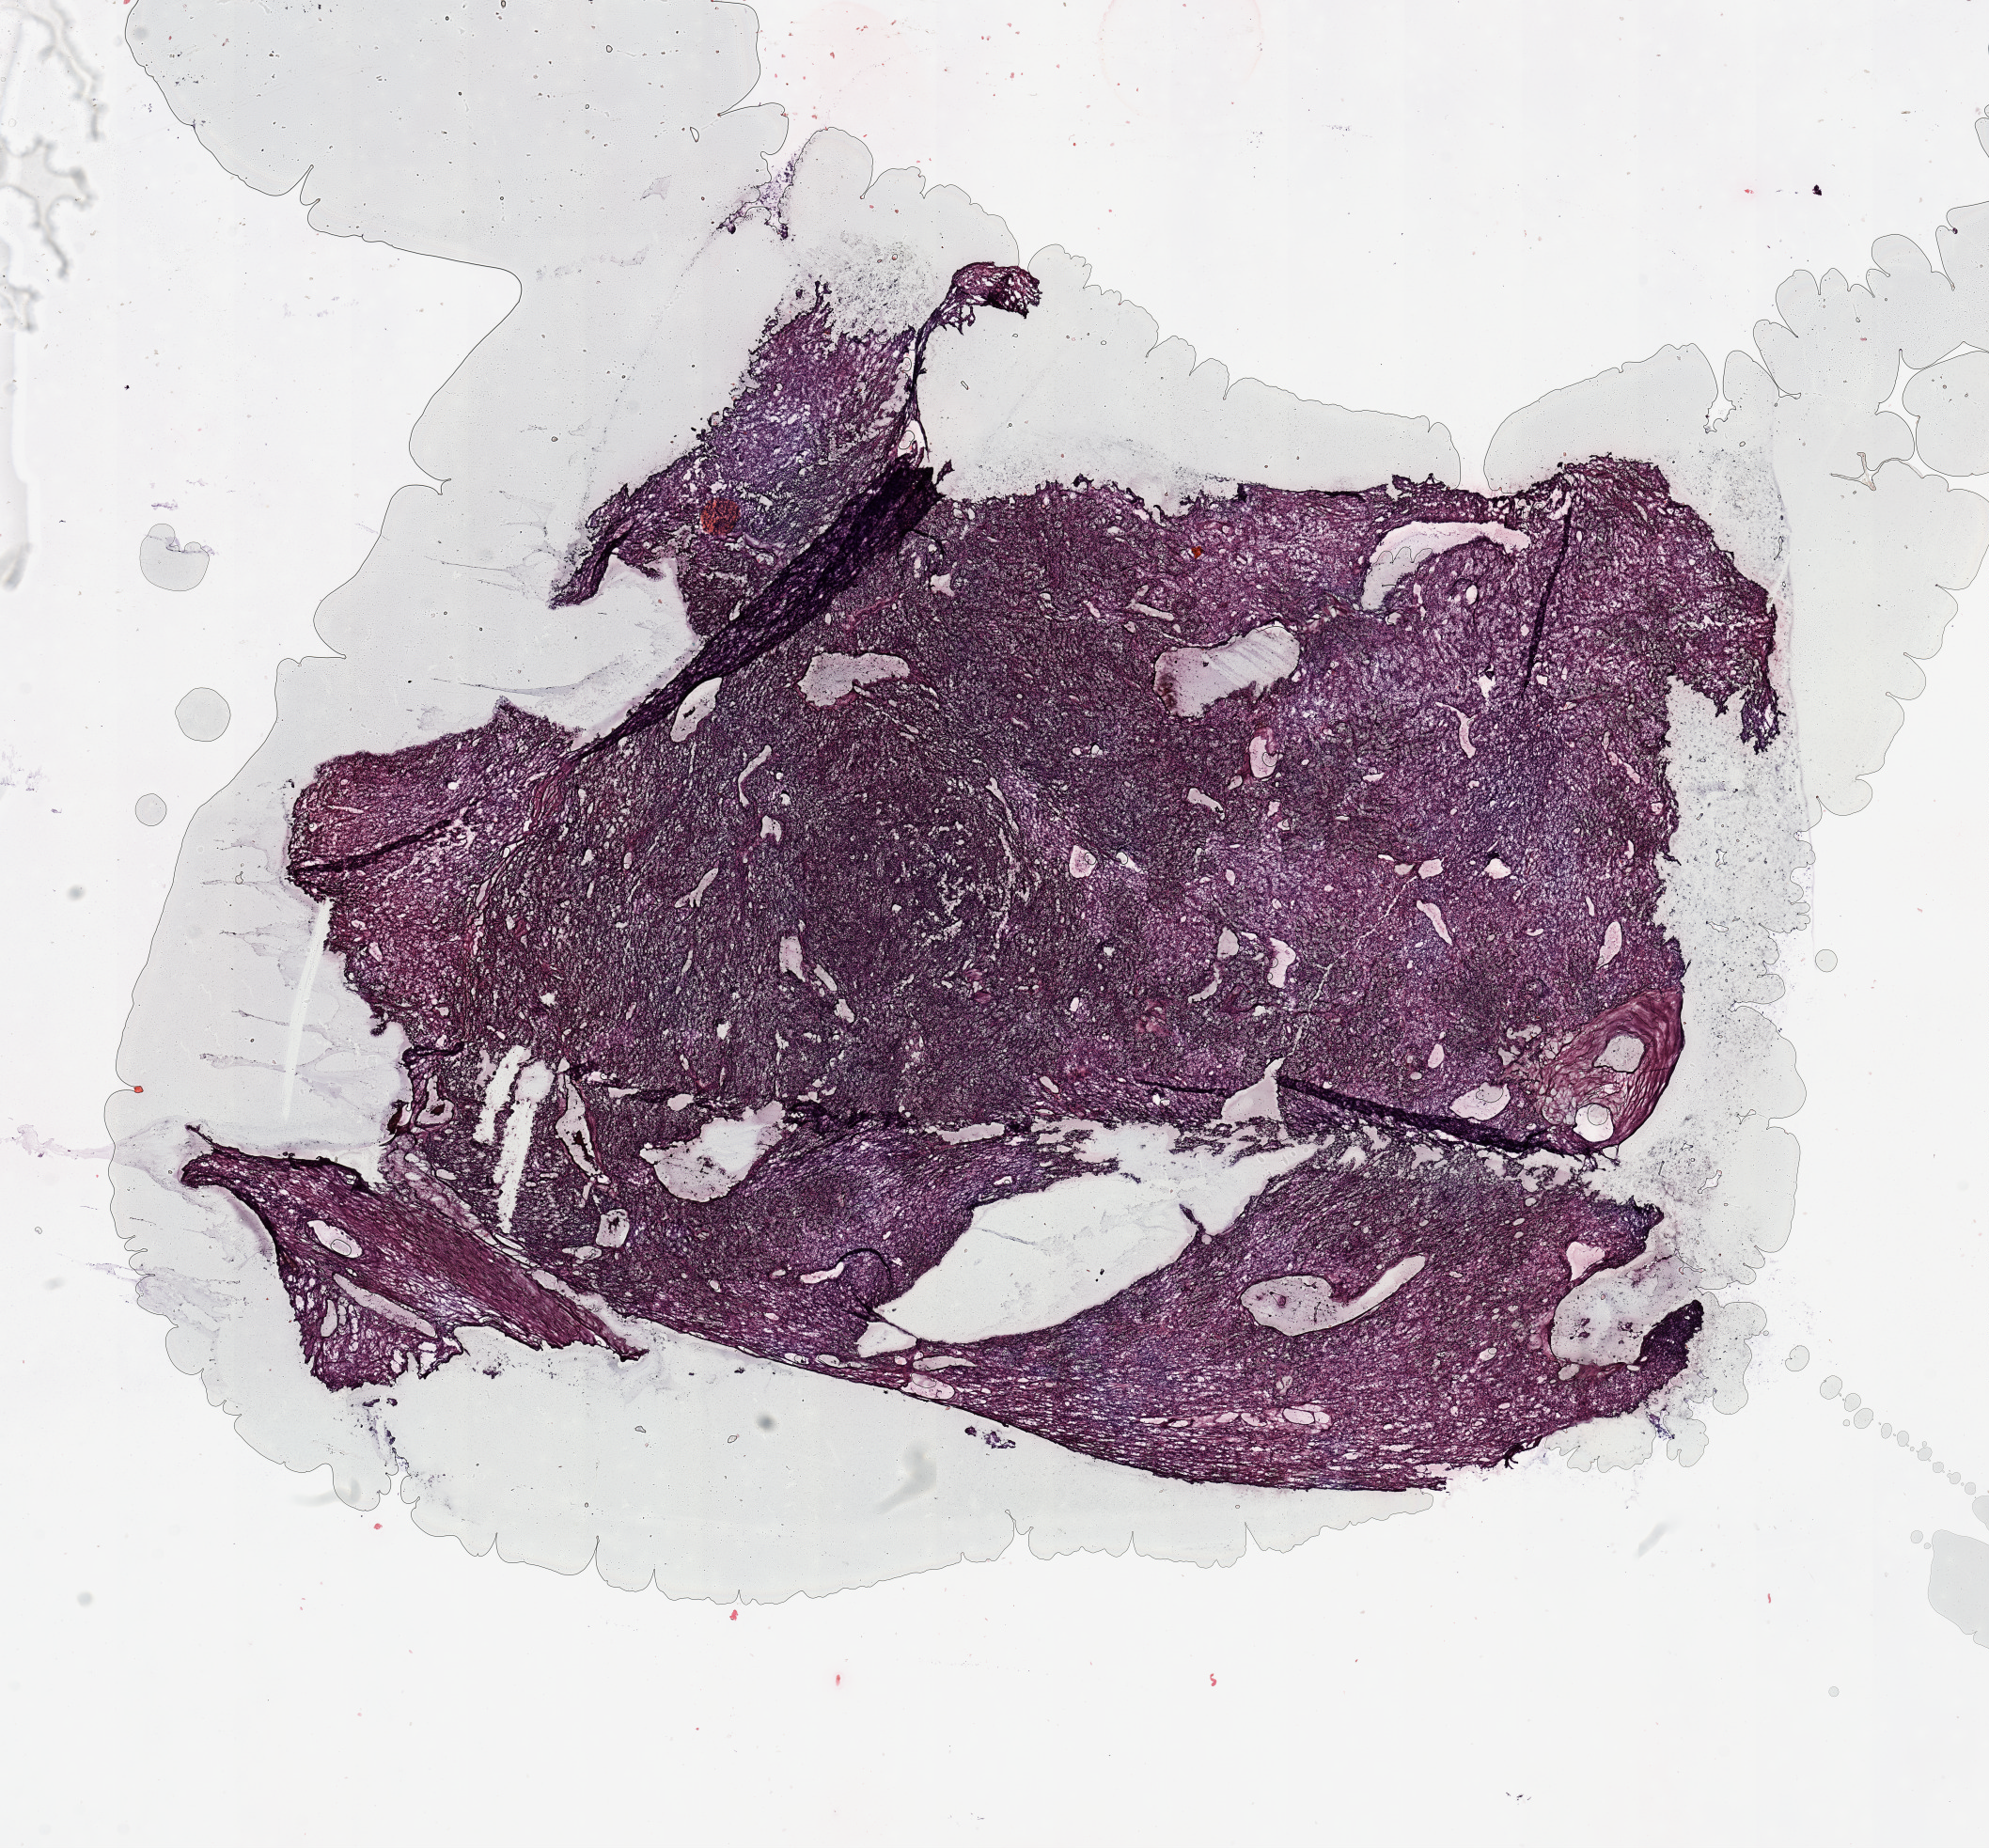
Digitized H&E-stained tissue section (whole slide) — a low-resolution overview of the entire scanned area, about 16.7 x 15.5 mm; tumour tissue sample, sampled site: kidney. 58-year-old male patient.
Histologic diagnosis: Renal cell carcinoma, NOS.